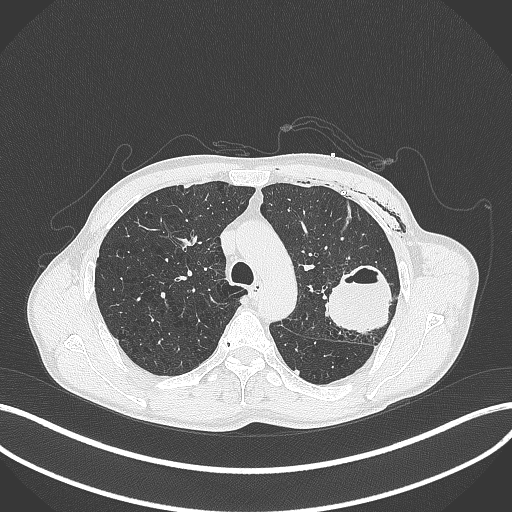
Chest CT, one axial slice. Slice 289 of 457 in the series (ordered by position). Reconstruction kernel B70f. Lung window (W 1500 / L -600 HU). 512 × 512 image matrix, field of view 400 × 400 mm. Patient: male, 58 years. Case-level facts recorded for this patient, not image findings: clinical TNM (as recorded): T3 N0 M0.
Annotated regions visible in this slice (rectangle marked by the reading radiologist):
- lung tumour (recorded histology: adenocarcinoma): bounding box (x1, y1, x2, y2) in pixels: (326, 261, 398, 336)